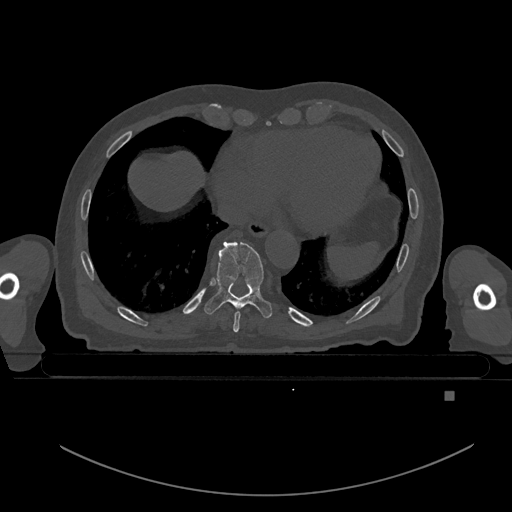
CT including the spine, one axial slice. Slice 155 of 969 in the series (ordered by position). Bone window (W 1800 / L 400 HU). 0.5 mm slice thickness. 512 × 512 image matrix, field of view 456 × 456 mm. Patient: male, 82 years. Case-level facts recorded for this patient, not image findings: primary cancer: prostate; vertebrae with lytic lesions (as recorded): T11, T9, T8, T2.
Outlined on this slice (semi-automatic segmentation, software-assisted and operator-edited):
- T8 vertebra: bounding box (x1, y1, x2, y2) in pixels: (233, 311, 241, 333)
- T9 vertebra: (204, 241, 272, 319)